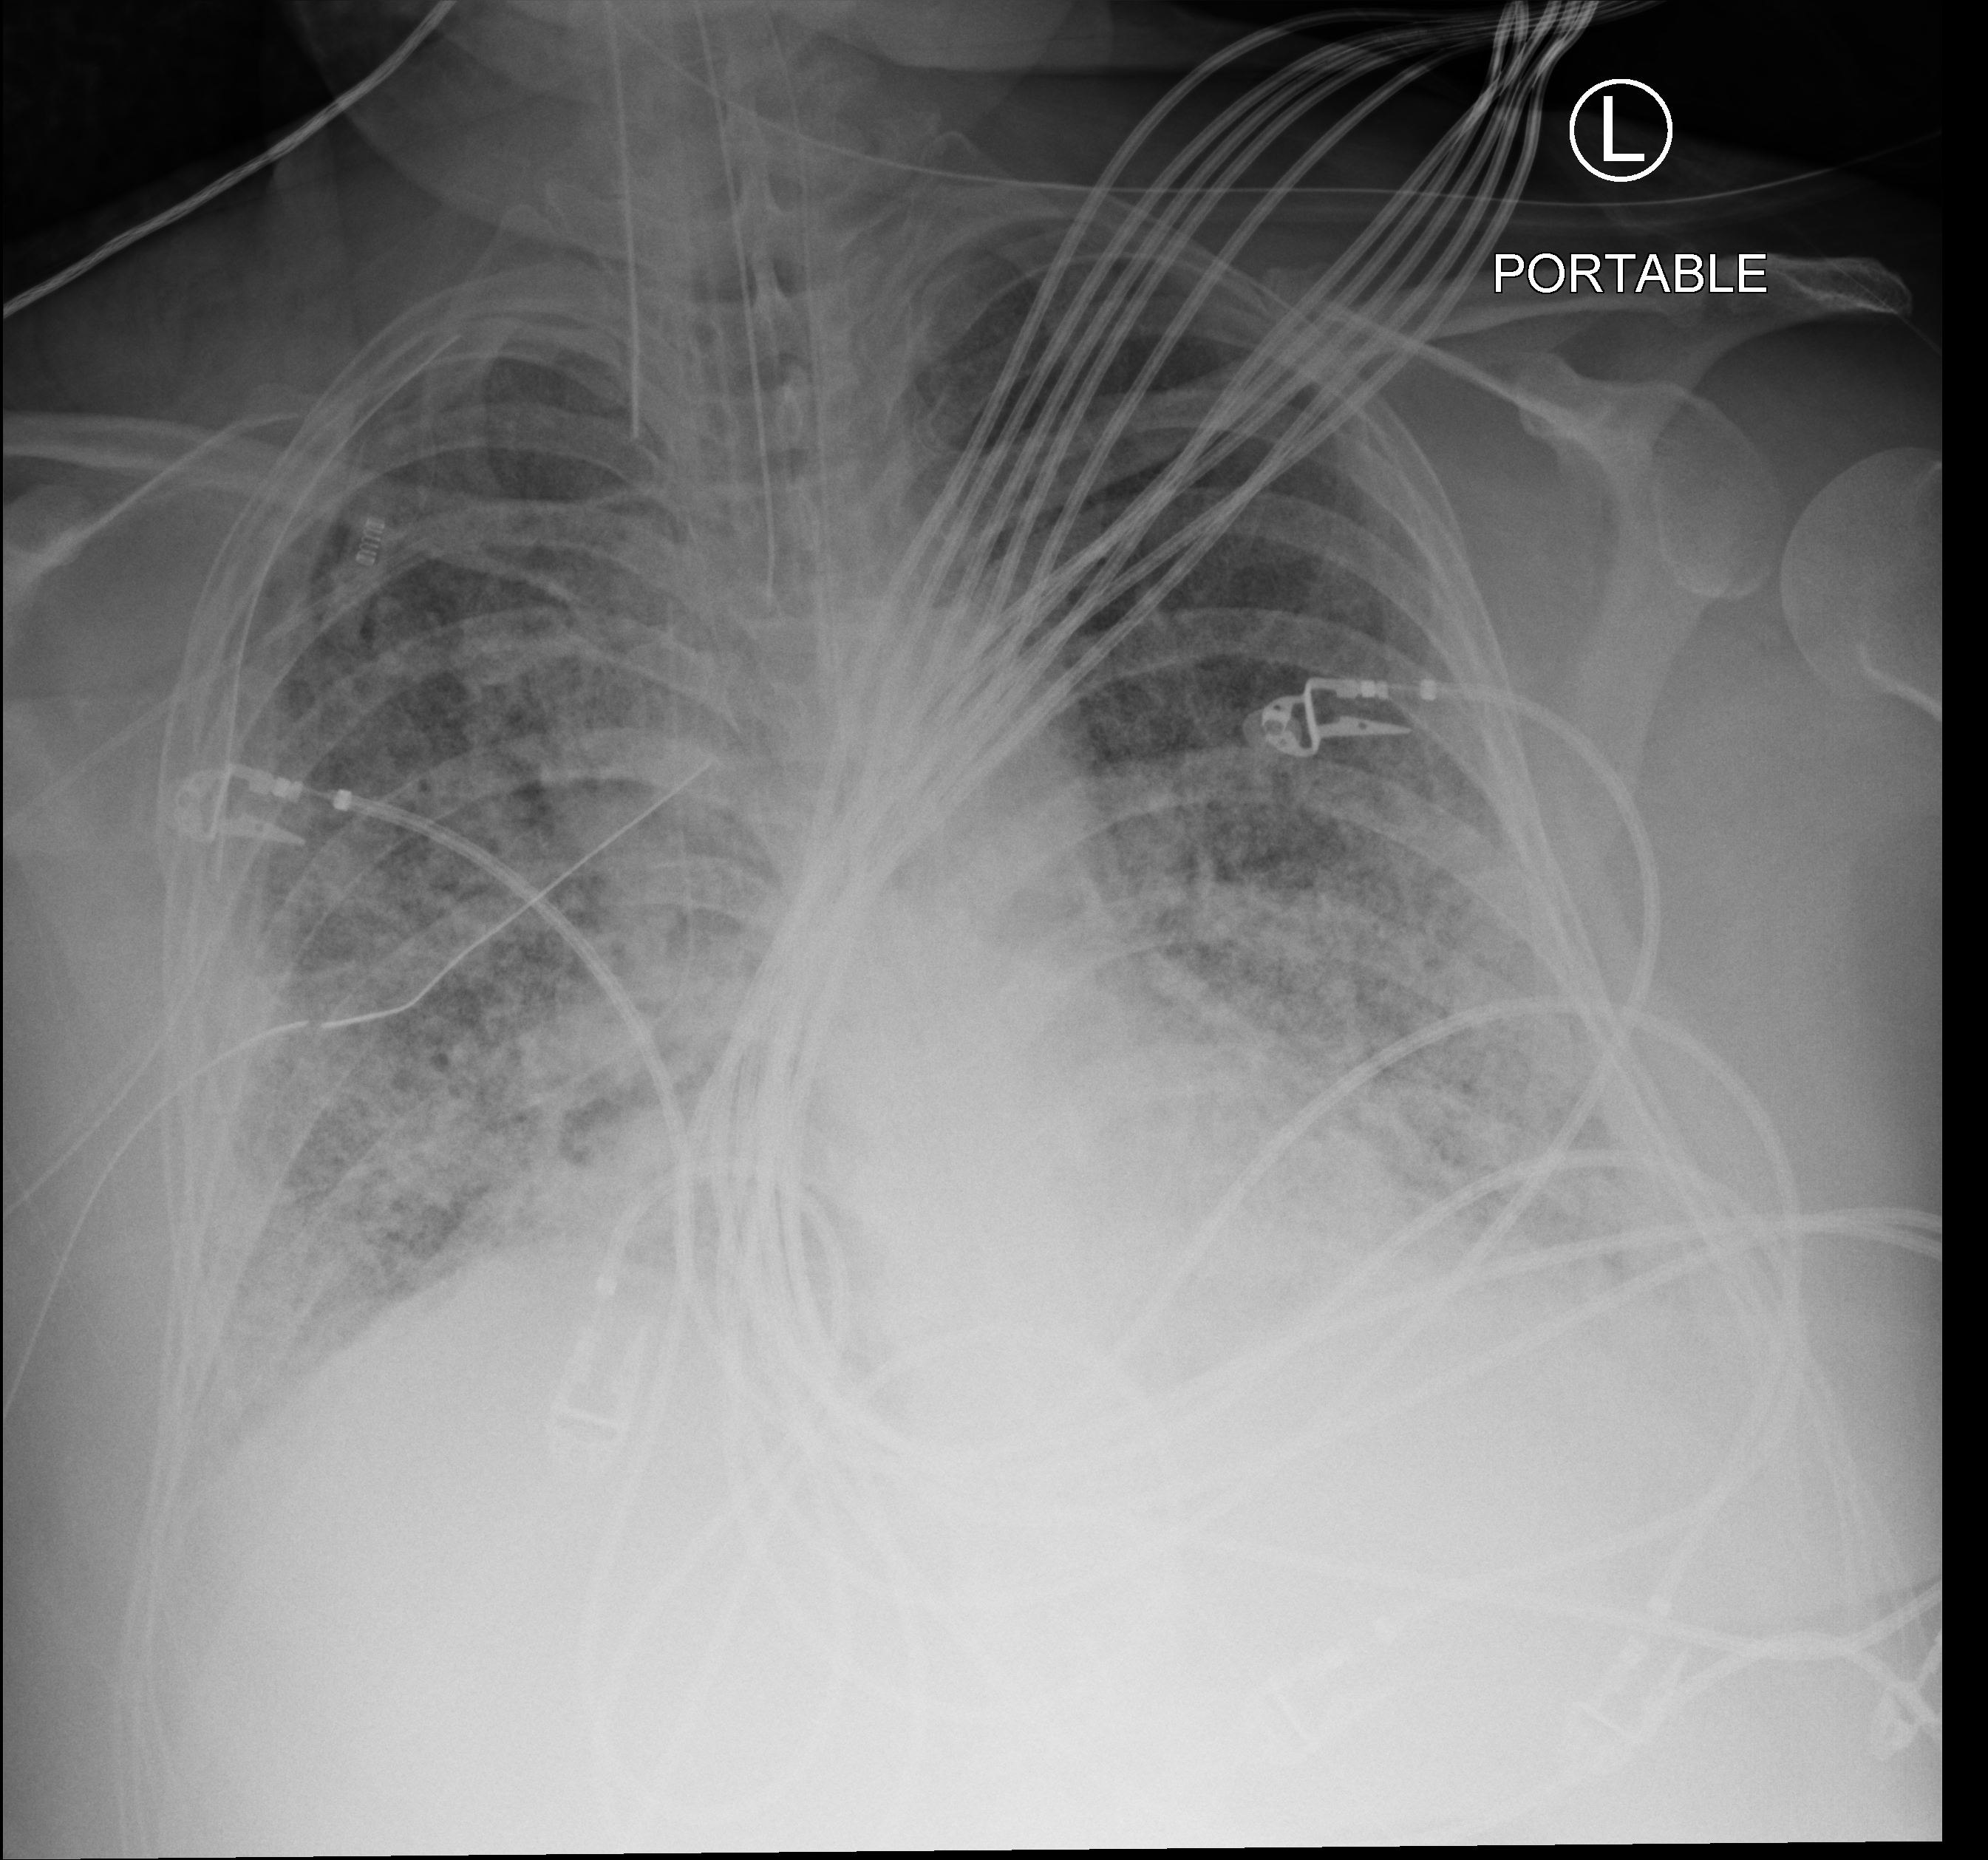
Chest X-ray (portable); anteroposterior (AP) projection. Adult patient hospitalised with COVID-19, age 18–59 years.
From the hospital-stay record, not from the radiograph (when in the stay this image was taken is not recorded): mechanically ventilated during this hospital stay: yes; length of hospital stay: 48 days; admitted to intensive care during this hospital stay: yes.